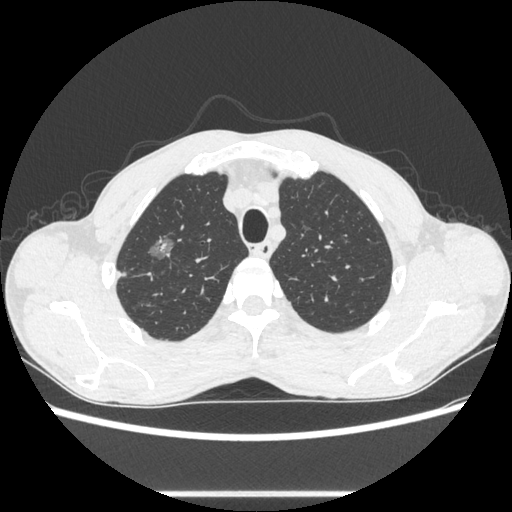
Chest CT, one axial slice. Position 490 of 600 along the scan axis. 100 kVp. Lung window (W 1500 / L -600 HU). 512 × 512 image matrix, field of view 357 × 357 mm. Patient: male, 54 years. Case-level facts recorded for this patient, not image findings: clinical TNM (as recorded): T1a N0 M0.
Annotated regions visible in this slice (rectangle marked by the reading radiologist):
- lung tumour (recorded histology: adenocarcinoma): bounding box [x1, y1, x2, y2] px = [137, 227, 181, 262]